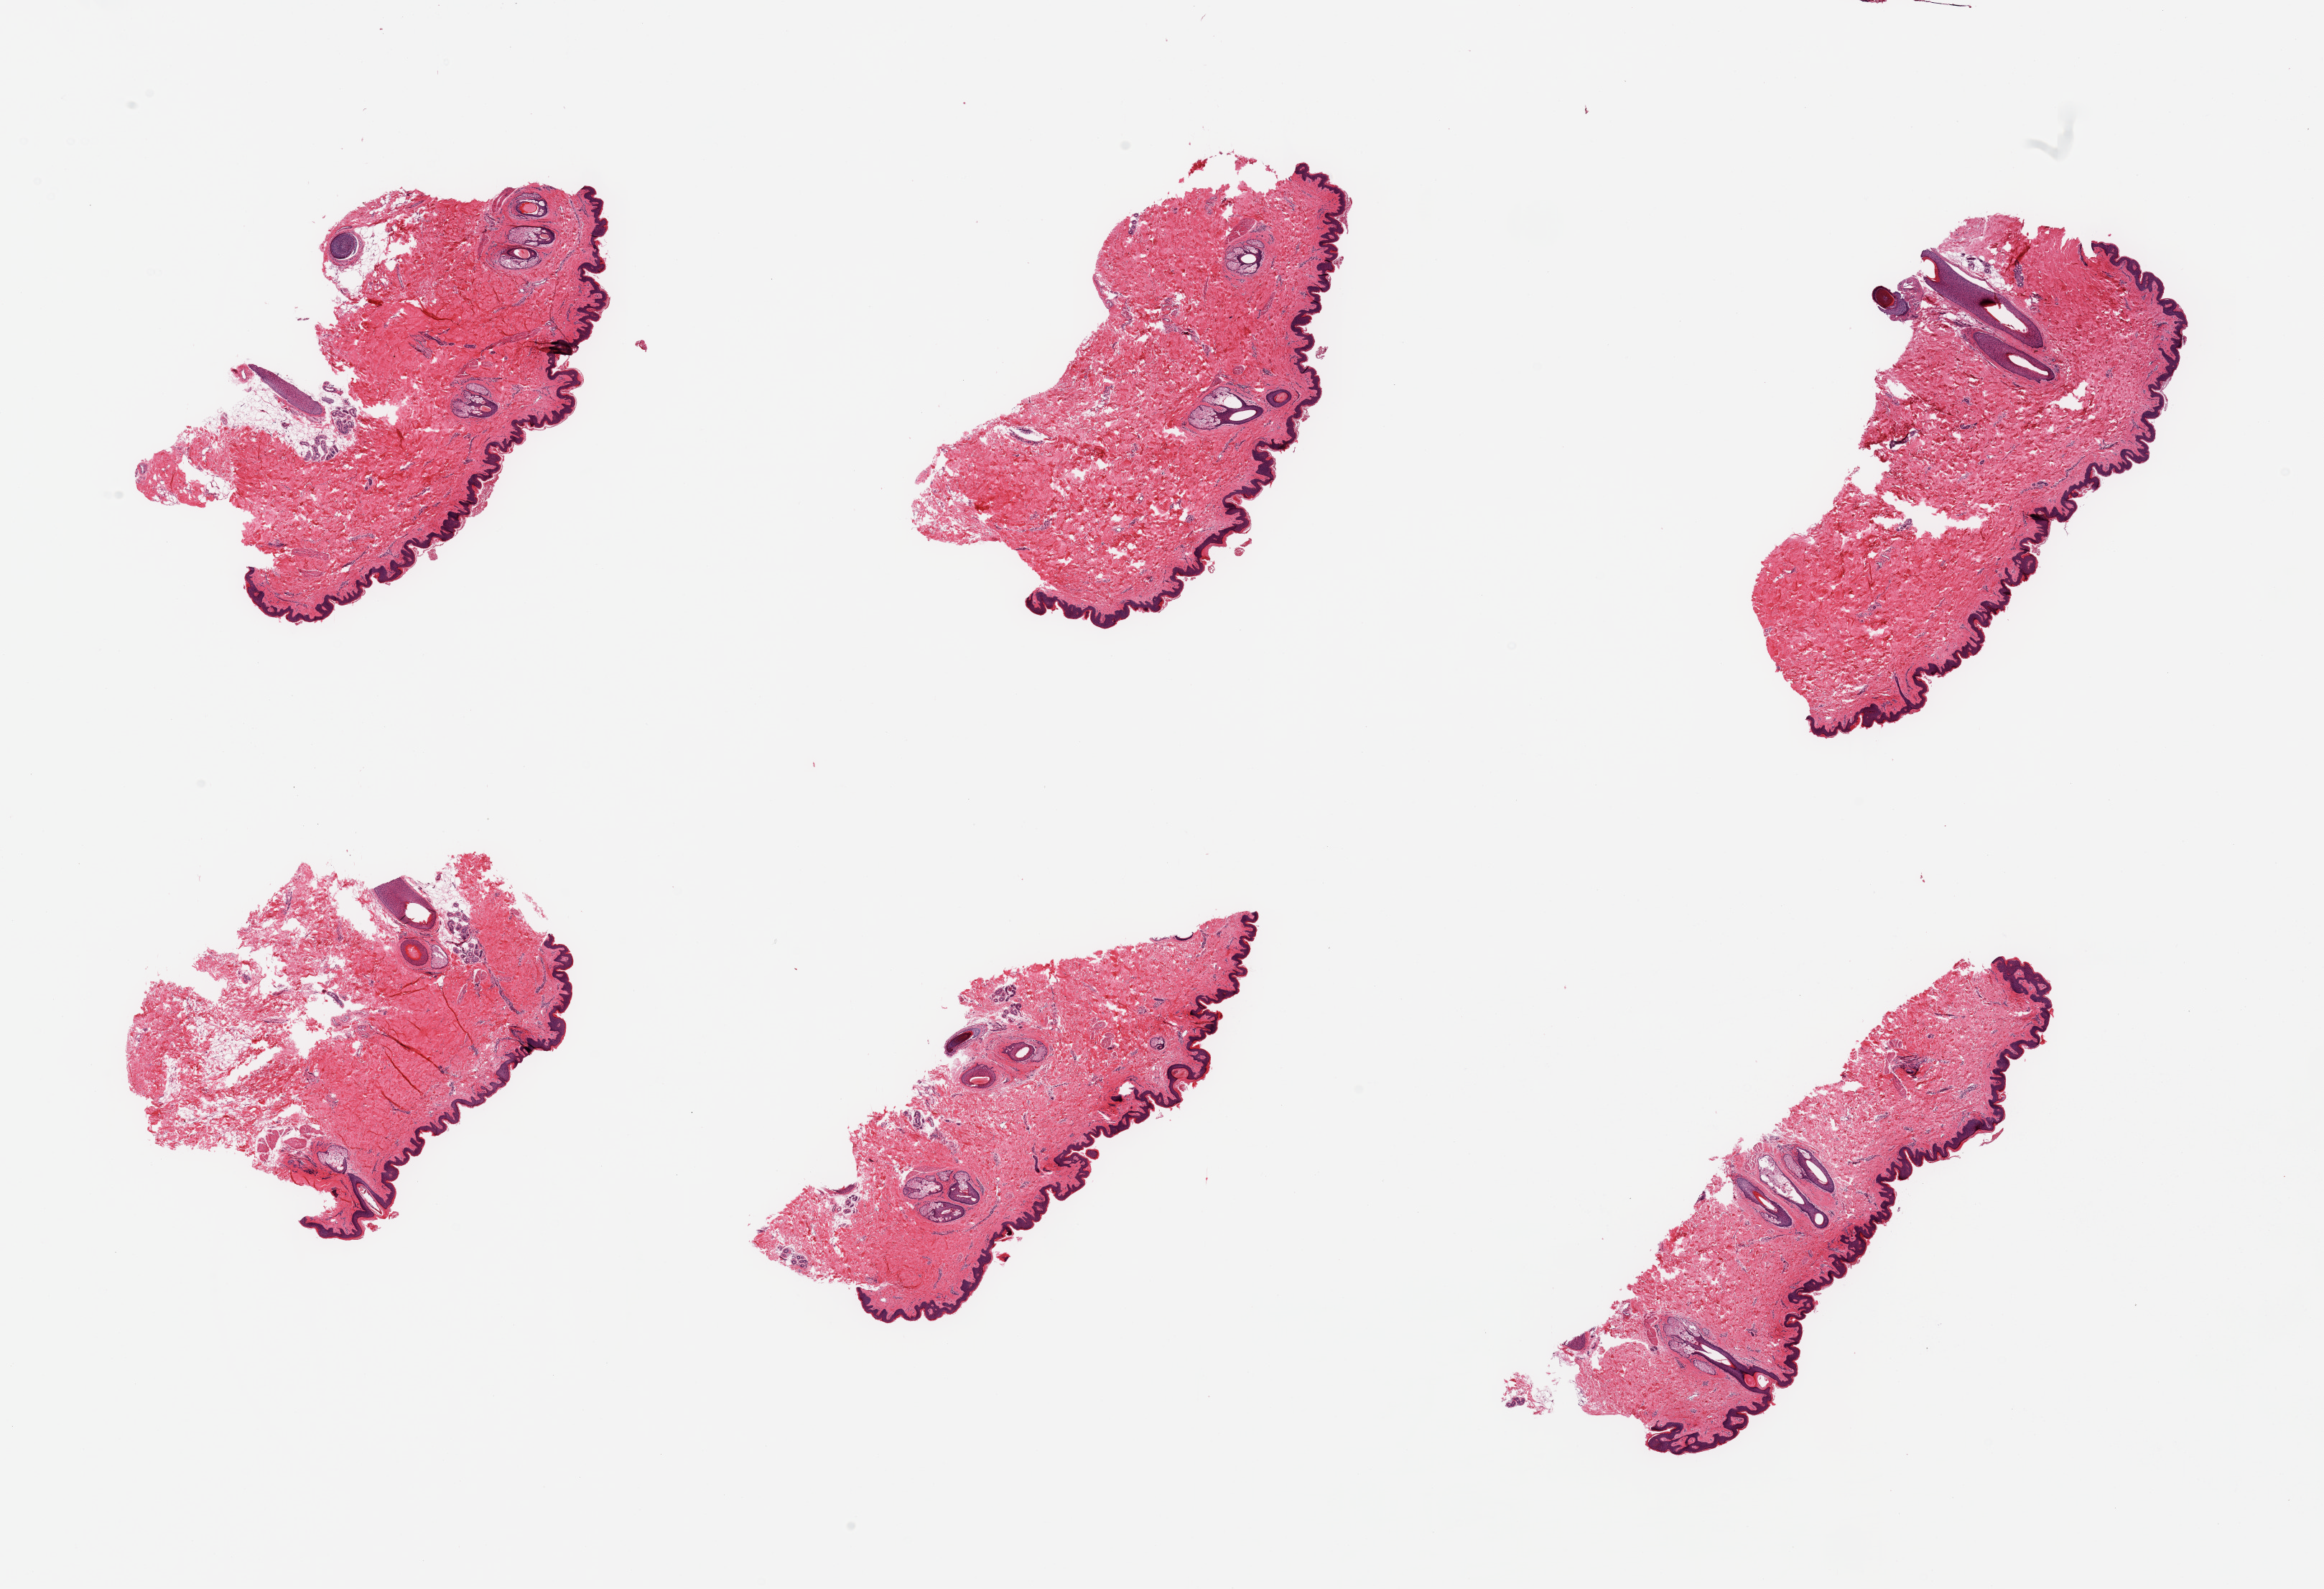
Digitized hematoxylin and eosin (H&E)-stained section, shown as a low-resolution overview of the whole scanned area (about 25.6 x 17.5 mm); PAXgene-fixed paraffin-embedded (PFPE) section; sampled site (target tissue): skin of suprapubic region; tissue donor sample. Donor sex: female.
Reviewer comment on this tissue sample: 6 pieces; up to 4 hair follicles on each piece; 5% dermal fat content.